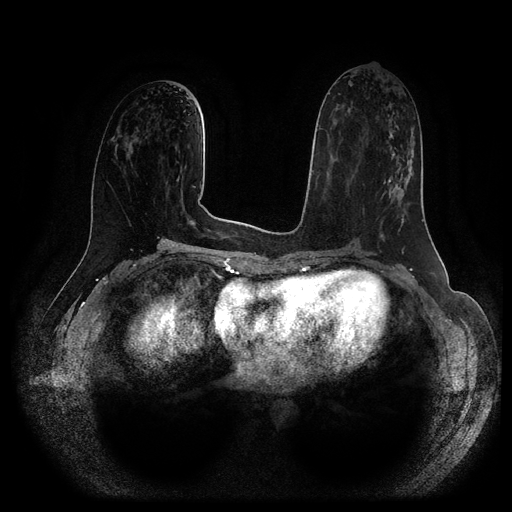
Breast MRI (dynamic contrast-enhanced, multi-phase), one axial slice. Position 48 of 116 along the scan axis. Dynamic contrast-enhanced series, time point 2 of 5 at this slice position (early post-contrast). 1.5 T. TE 2.6 ms, TR 5.2 ms. 2 mm slice thickness. 512 × 512 image matrix, field of view 380 × 380 mm. Female patient, age 57 years.
Outlined on this slice (semi-automatically segmented with operator editing):
- breast lesion (labelled 'tumour' in the annotation; benign lesions carry a separate 'benign' label): box from (x=382, y=131) to (x=414, y=204) px